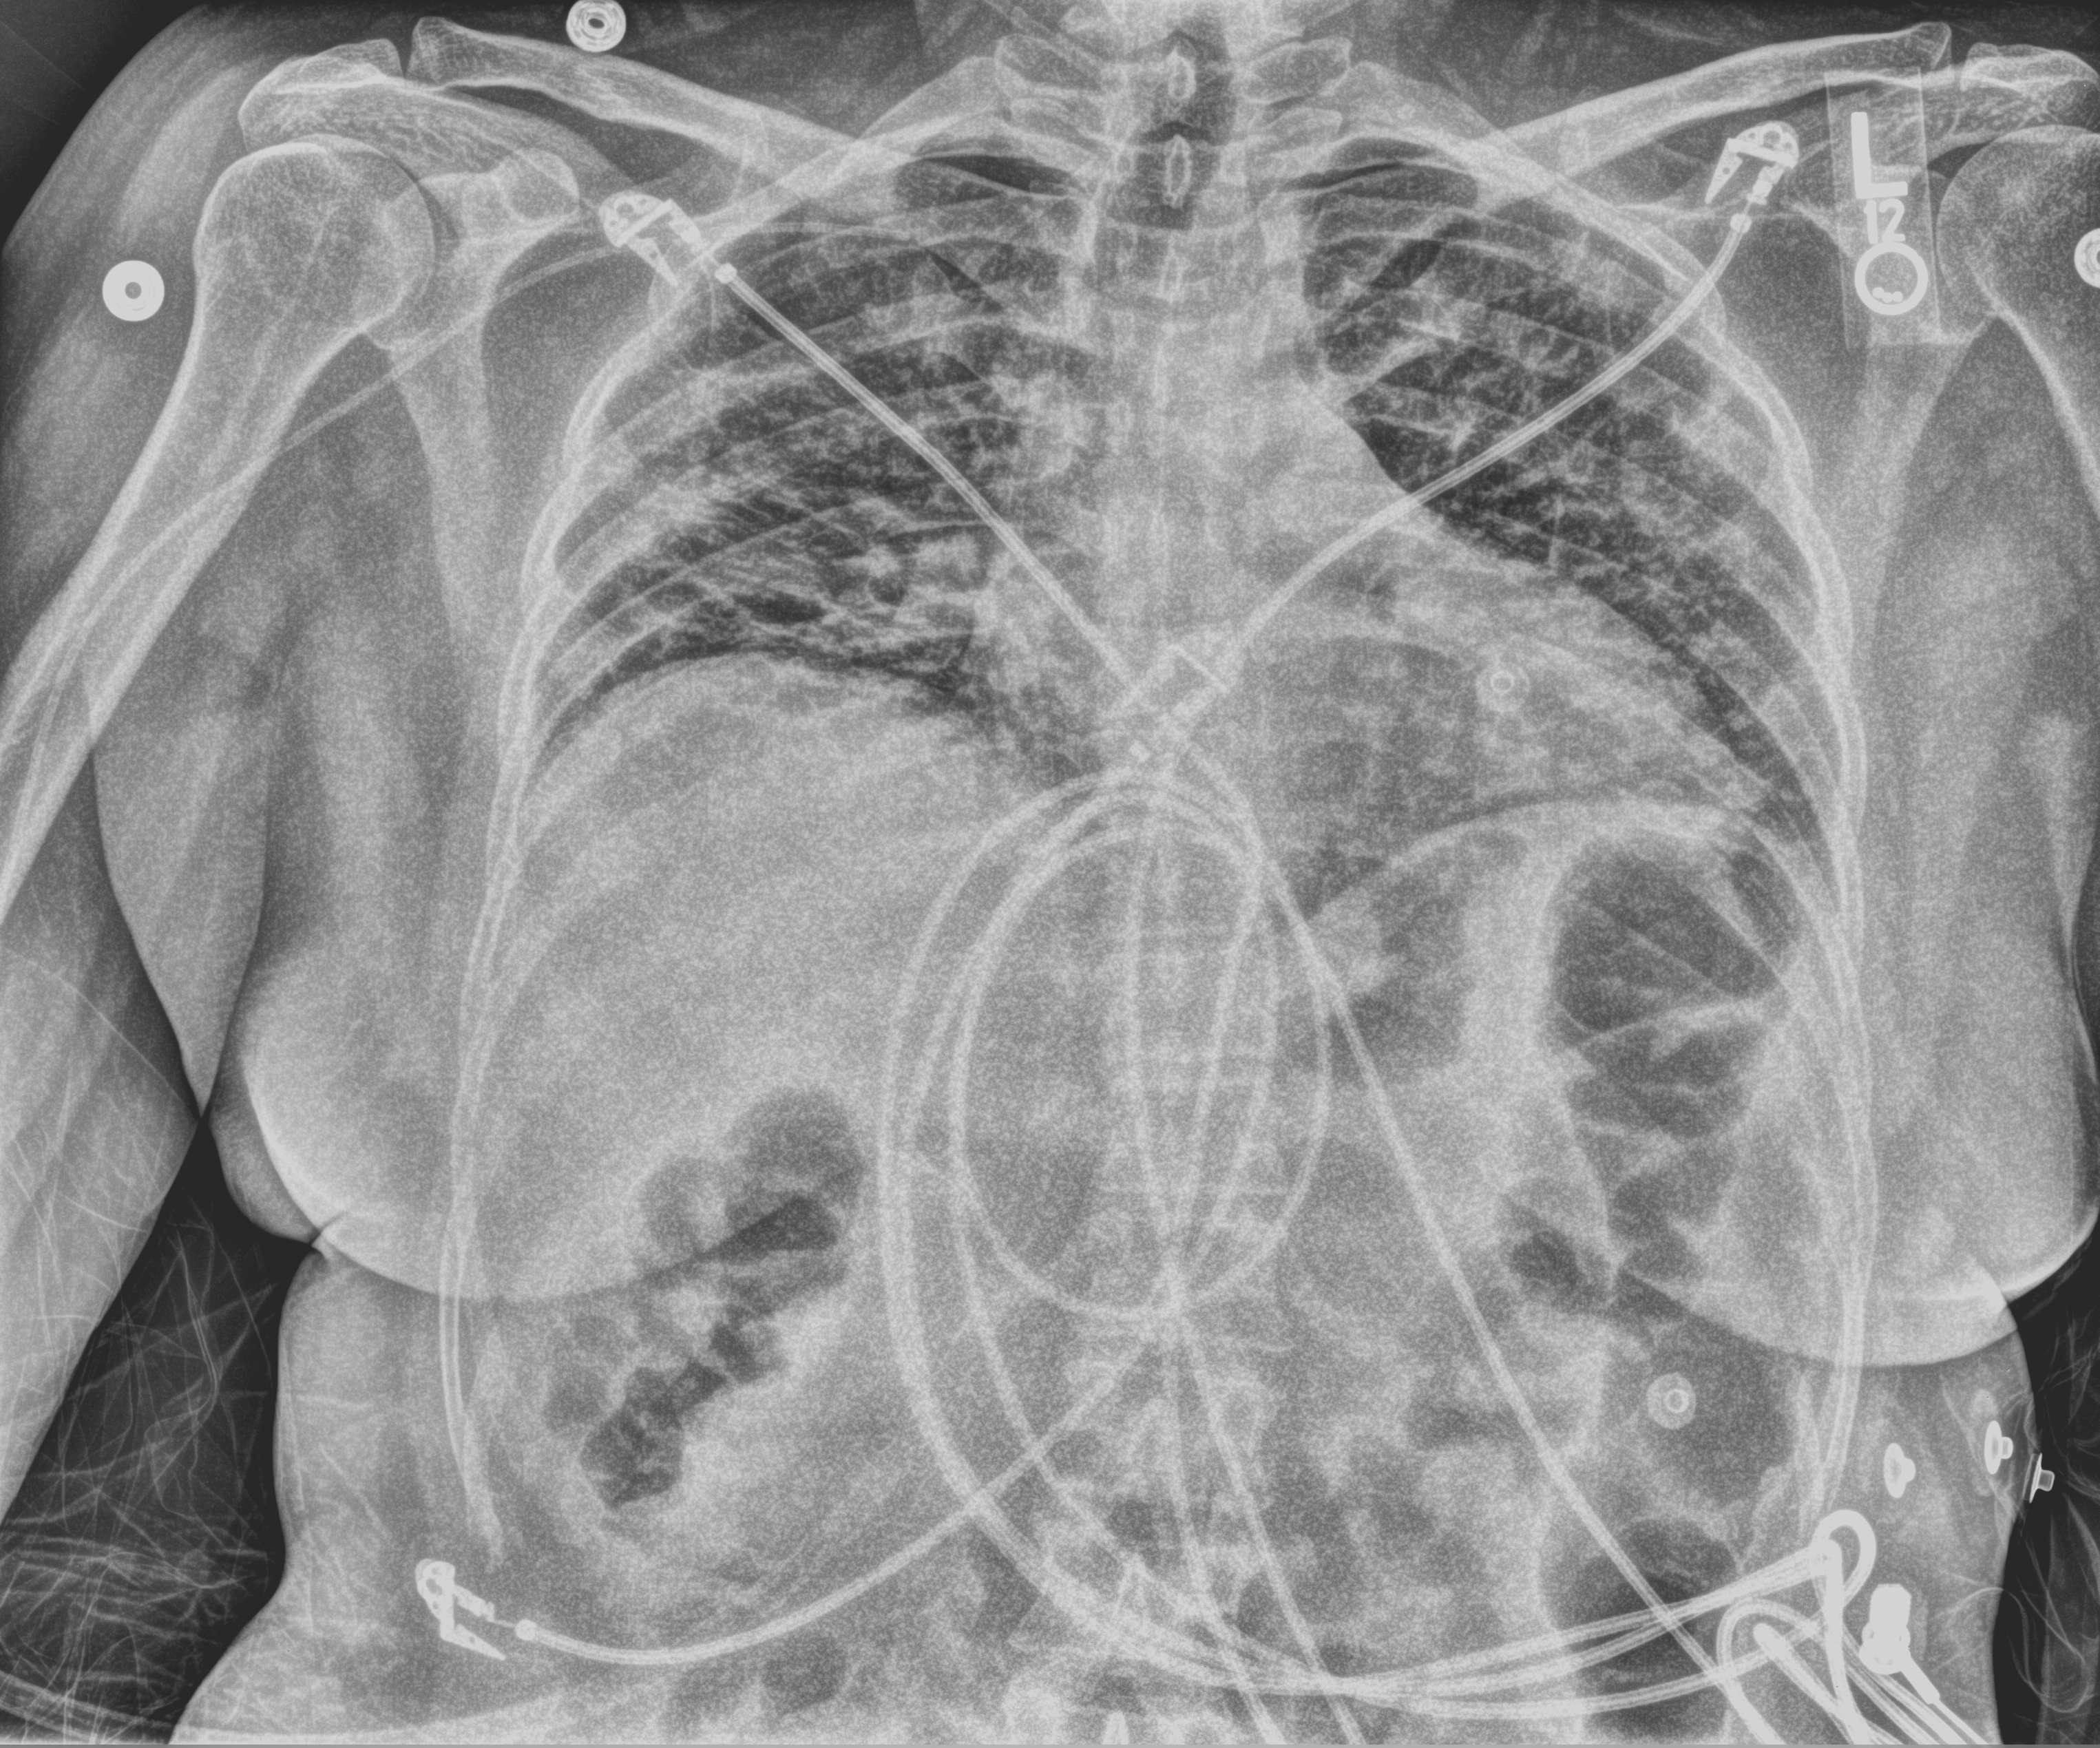
Portable chest radiograph, anteroposterior (AP) projection. Patient hospitalised with COVID-19; female, aged 18–59 years.
From the hospital-stay record, not from the radiograph (when in the stay this image was taken is not recorded): admitted to intensive care during this hospital stay: yes; mechanically ventilated during this hospital stay: yes.